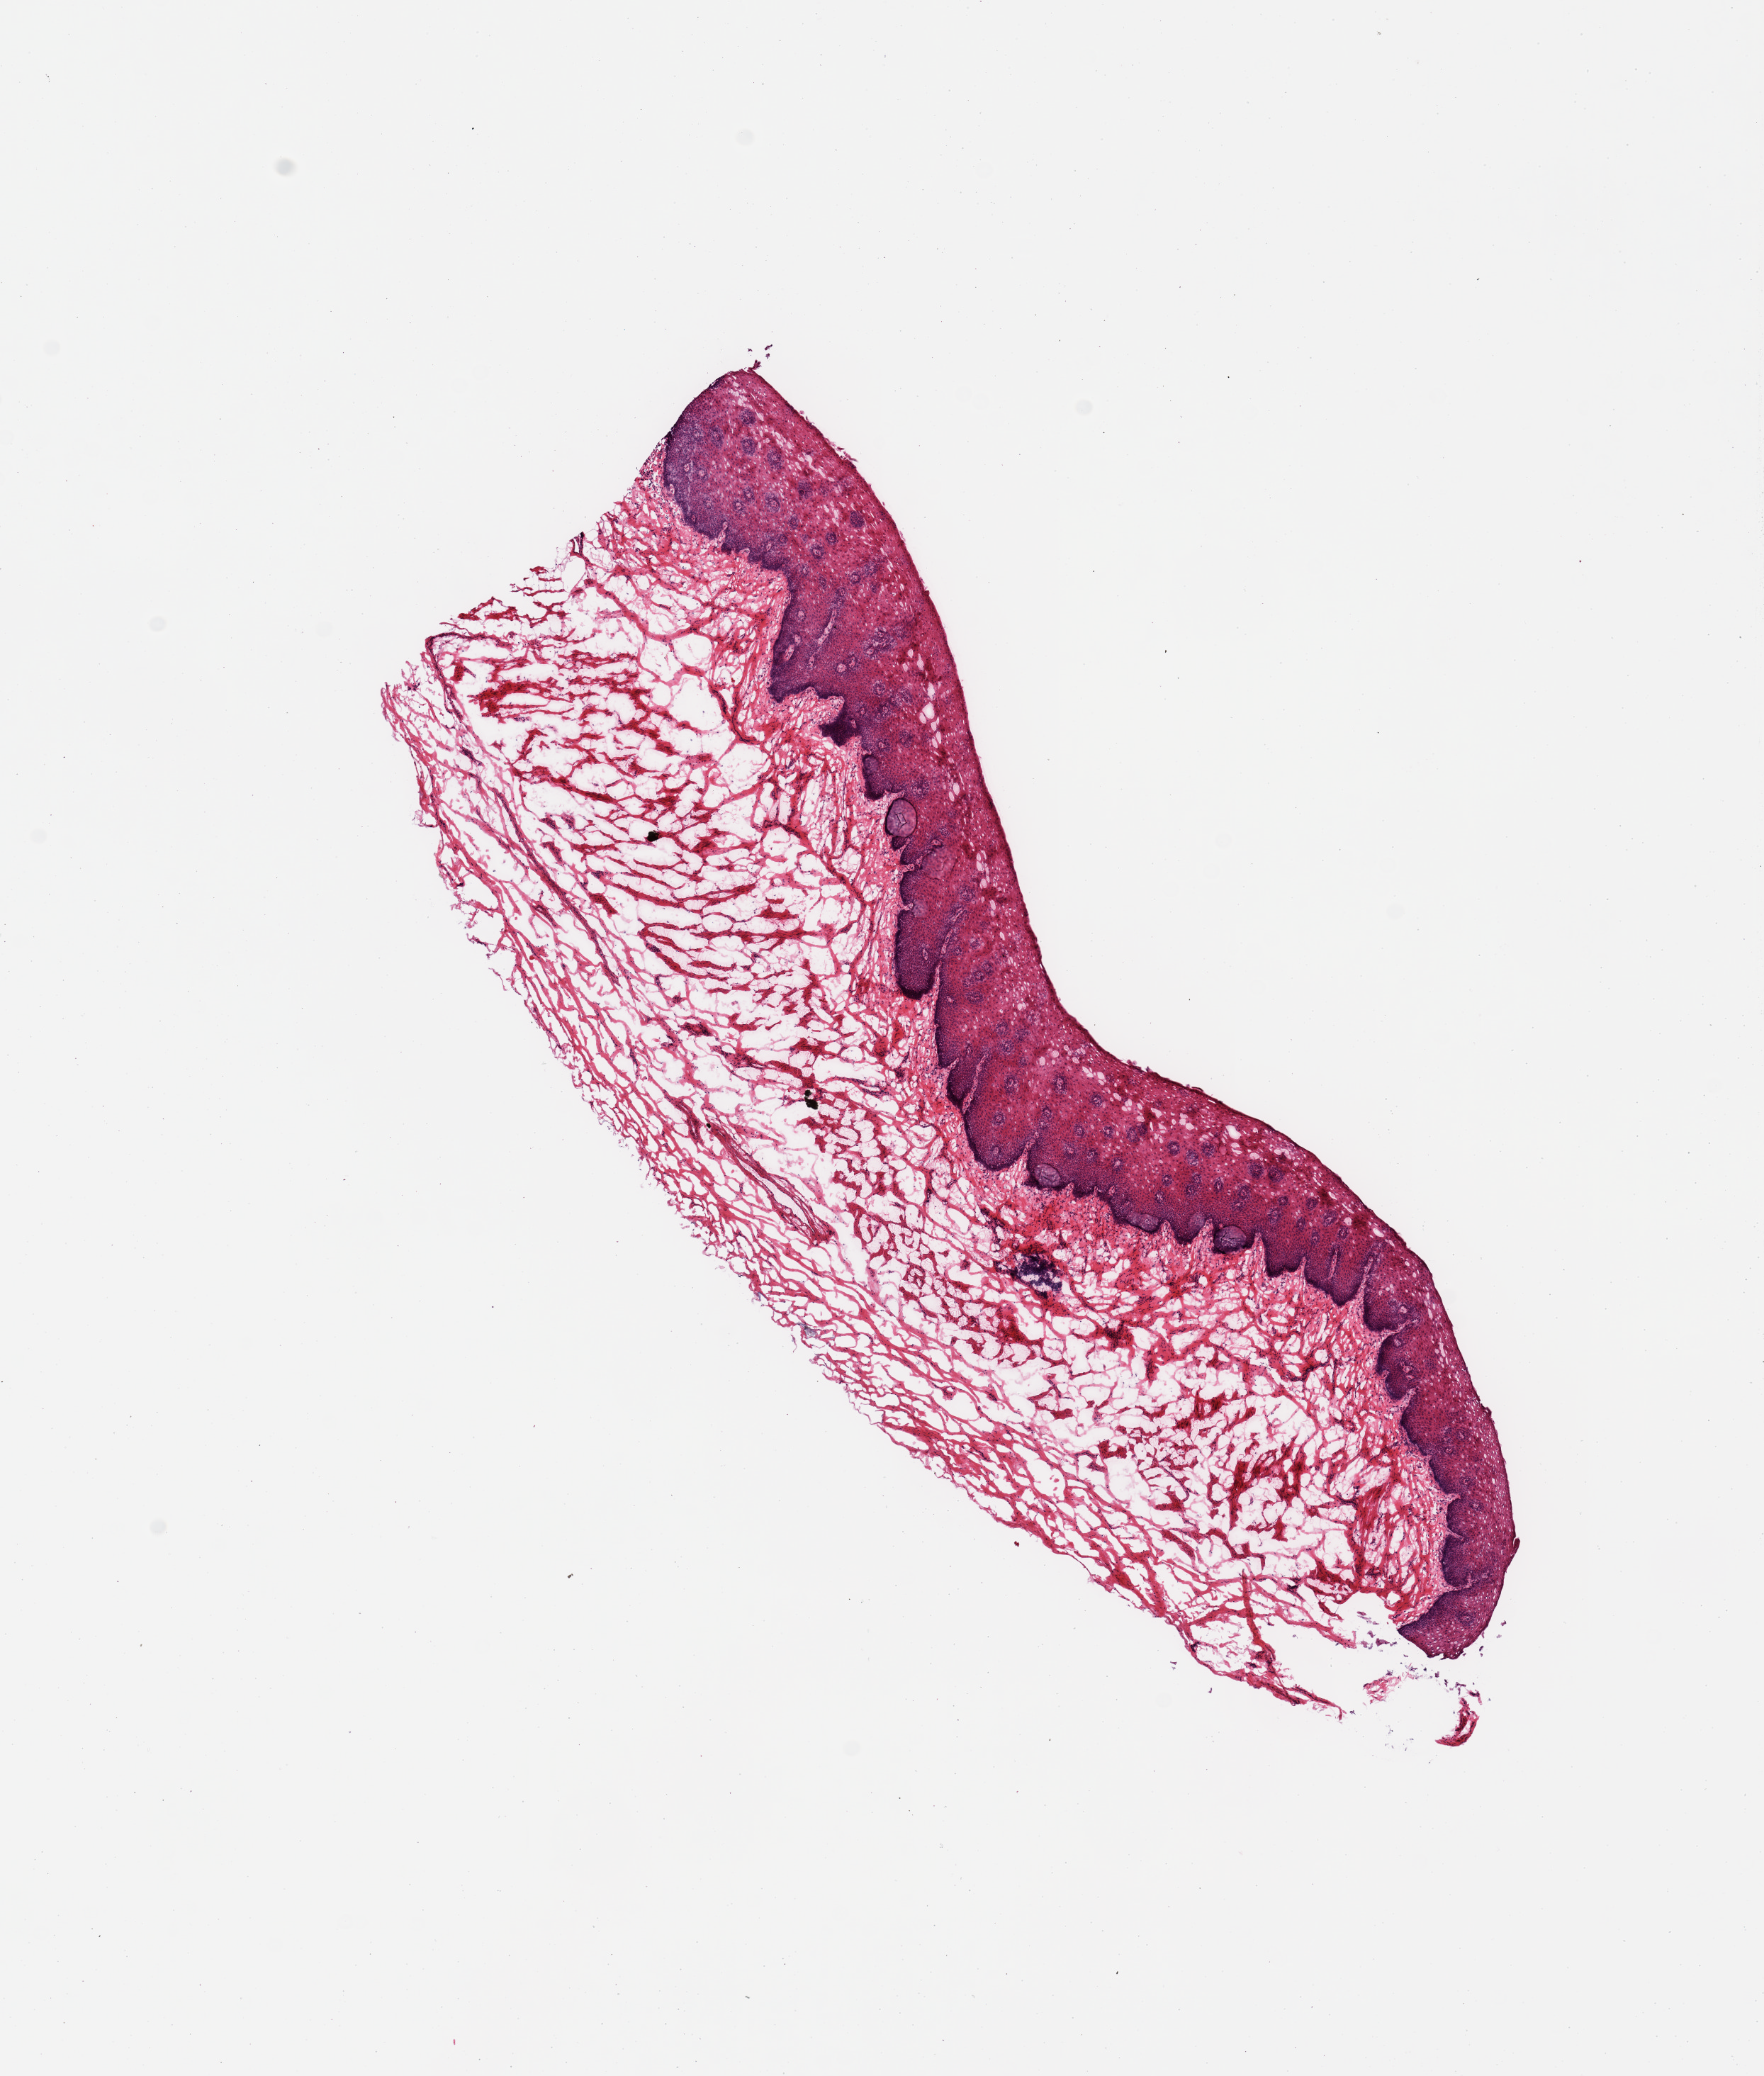
H&E whole-slide image, brightfield, whole scanned area (about 9.8 x 11.6 mm, acquisition: 20x scan) shown as a low-resolution overview.
- specimen: frozen section; section of esophageal mucous membrane (target tissue); tissue donor sample